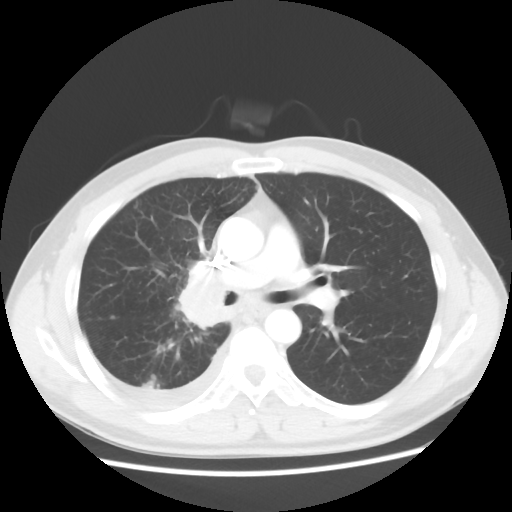
Chest CT, one axial slice. Position 32 of 56 along the scan axis. Reconstruction kernel STANDARD. 120 kVp. Lung window (W 1500 / L -600 HU). 5 mm slice thickness. 512 × 512 image matrix, field of view 360 × 360 mm. Male patient, age 46 years. Case-level facts recorded for this patient, not image findings: clinical TNM (as recorded): T2 N3 M1.
Annotated regions visible in this slice (bounding box drawn by a radiologist):
- lung tumour (recorded histology: adenocarcinoma): bounding box <176,259,227,337> (left, top, right, bottom; pixels)